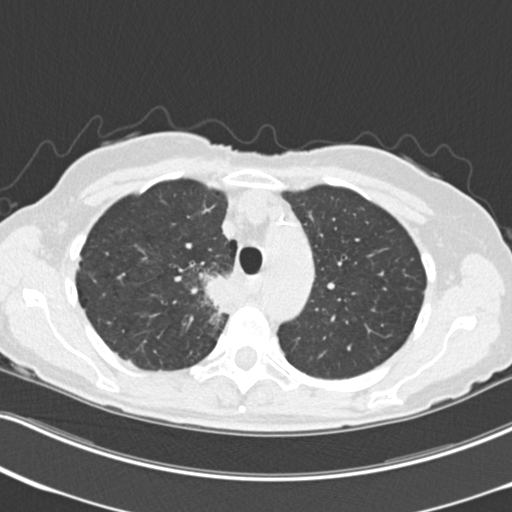
Chest CT (low-dose screening protocol), one axial image, third annual screen, lung window (W 1500 / L -600 HU), slice 56 of 226 in the series. Female participant, aged 68 years at enrolment. Current smoker at enrolment.
Expert-annotated lung lesion, bounding box [x1, y1, x2, y2] px = [196, 267, 249, 323]. Screening reader's record for this exam (one nodule recorded; not confirmed to be the boxed lesion): non-calcified nodule or mass ≥4 mm, right upper lobe, 31 × 29 mm, poorly defined margins, soft tissue attenuation, pre-existing on the prior screen: no. Official screen result: positive, other.